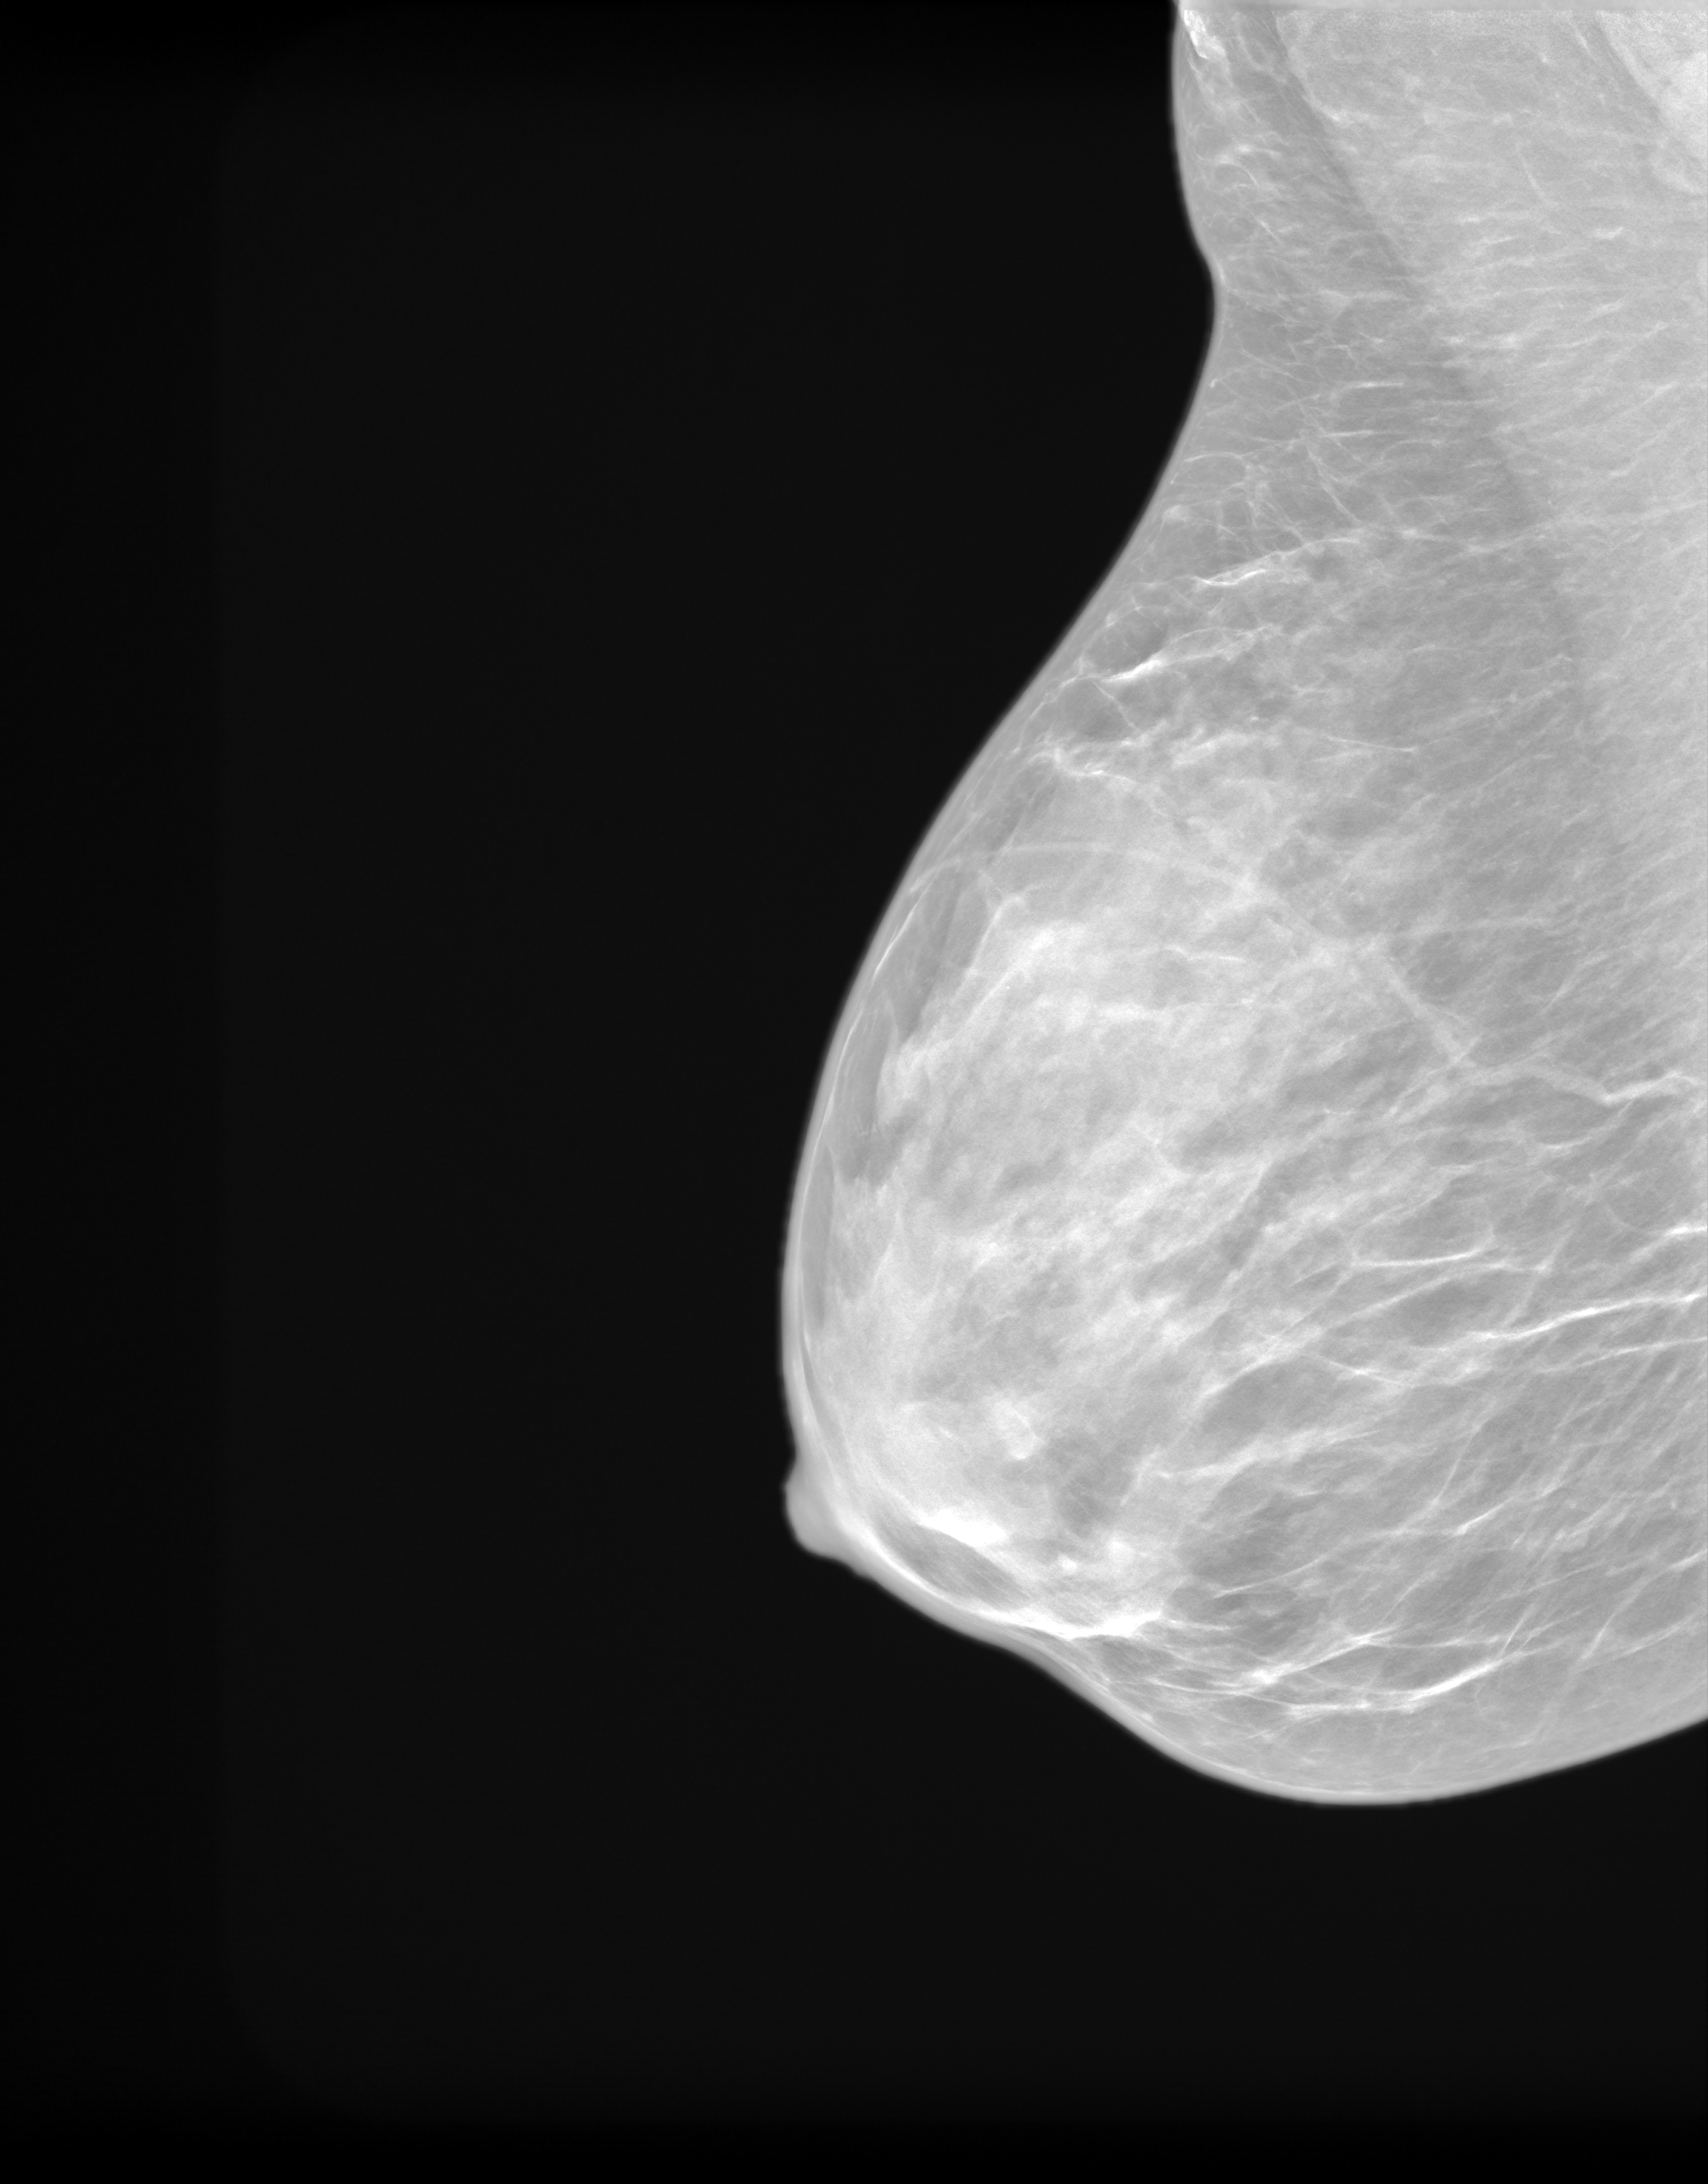
Annual screening mammography examination. Female patient, age 49 years.
Image type: synthesized 2-D view from tomosynthesis. Breast: right. Projection: MLO view.